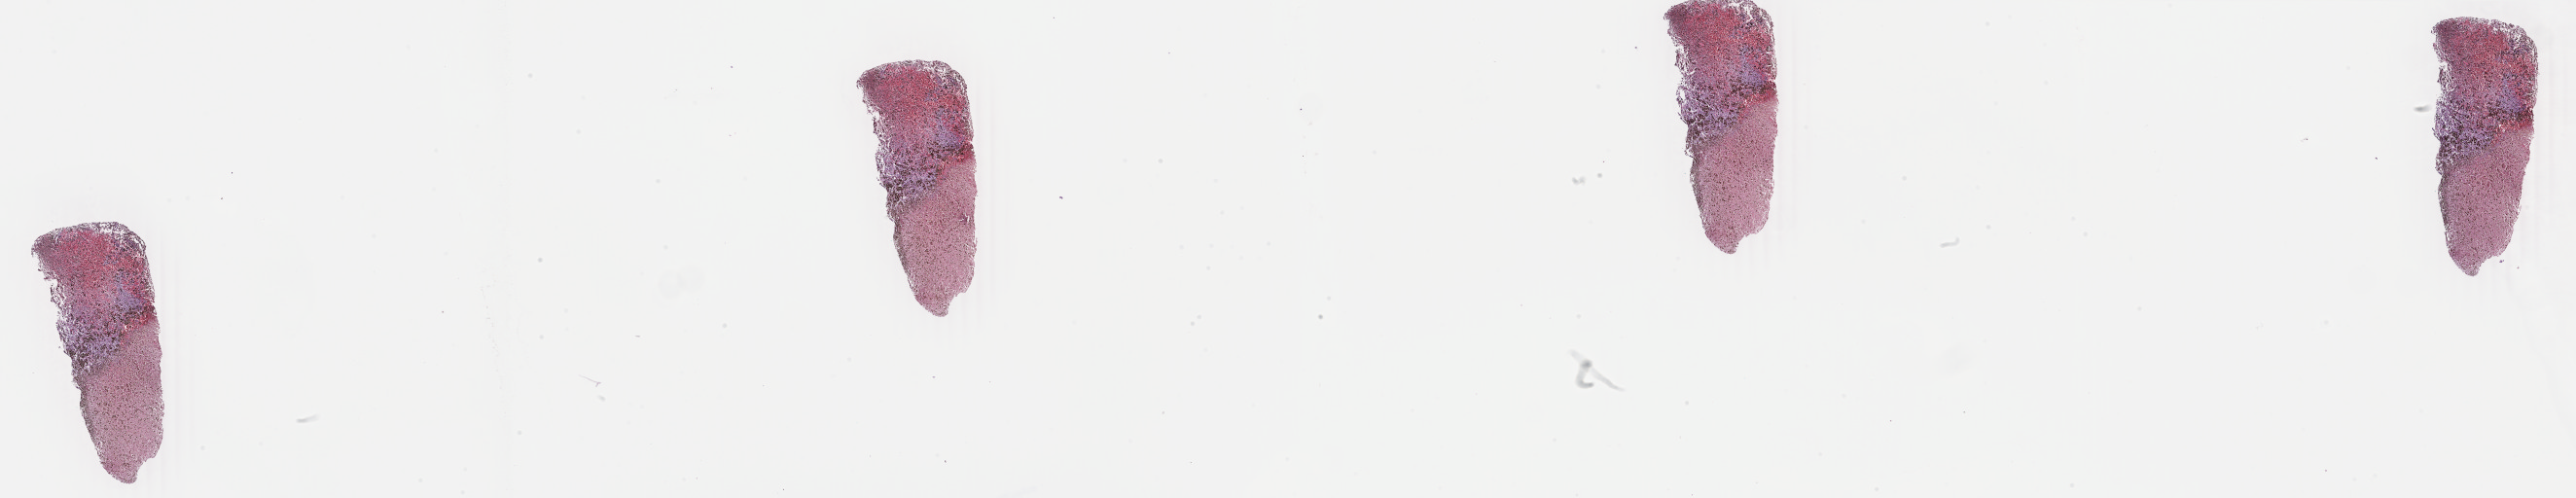
Digitized Hematoxylin and eosin (H&E) stained tissue section (whole slide), shown as a low-resolution overview of the whole scanned area (about 42.1 x 8.1 mm), formalin-fixed paraffin-embedded (FFPE) diagnostic section, primary tumour sample from the skin. Male patient; age at initial diagnosis 73 years.
Histologic diagnosis: Malignant melanoma, NOS.